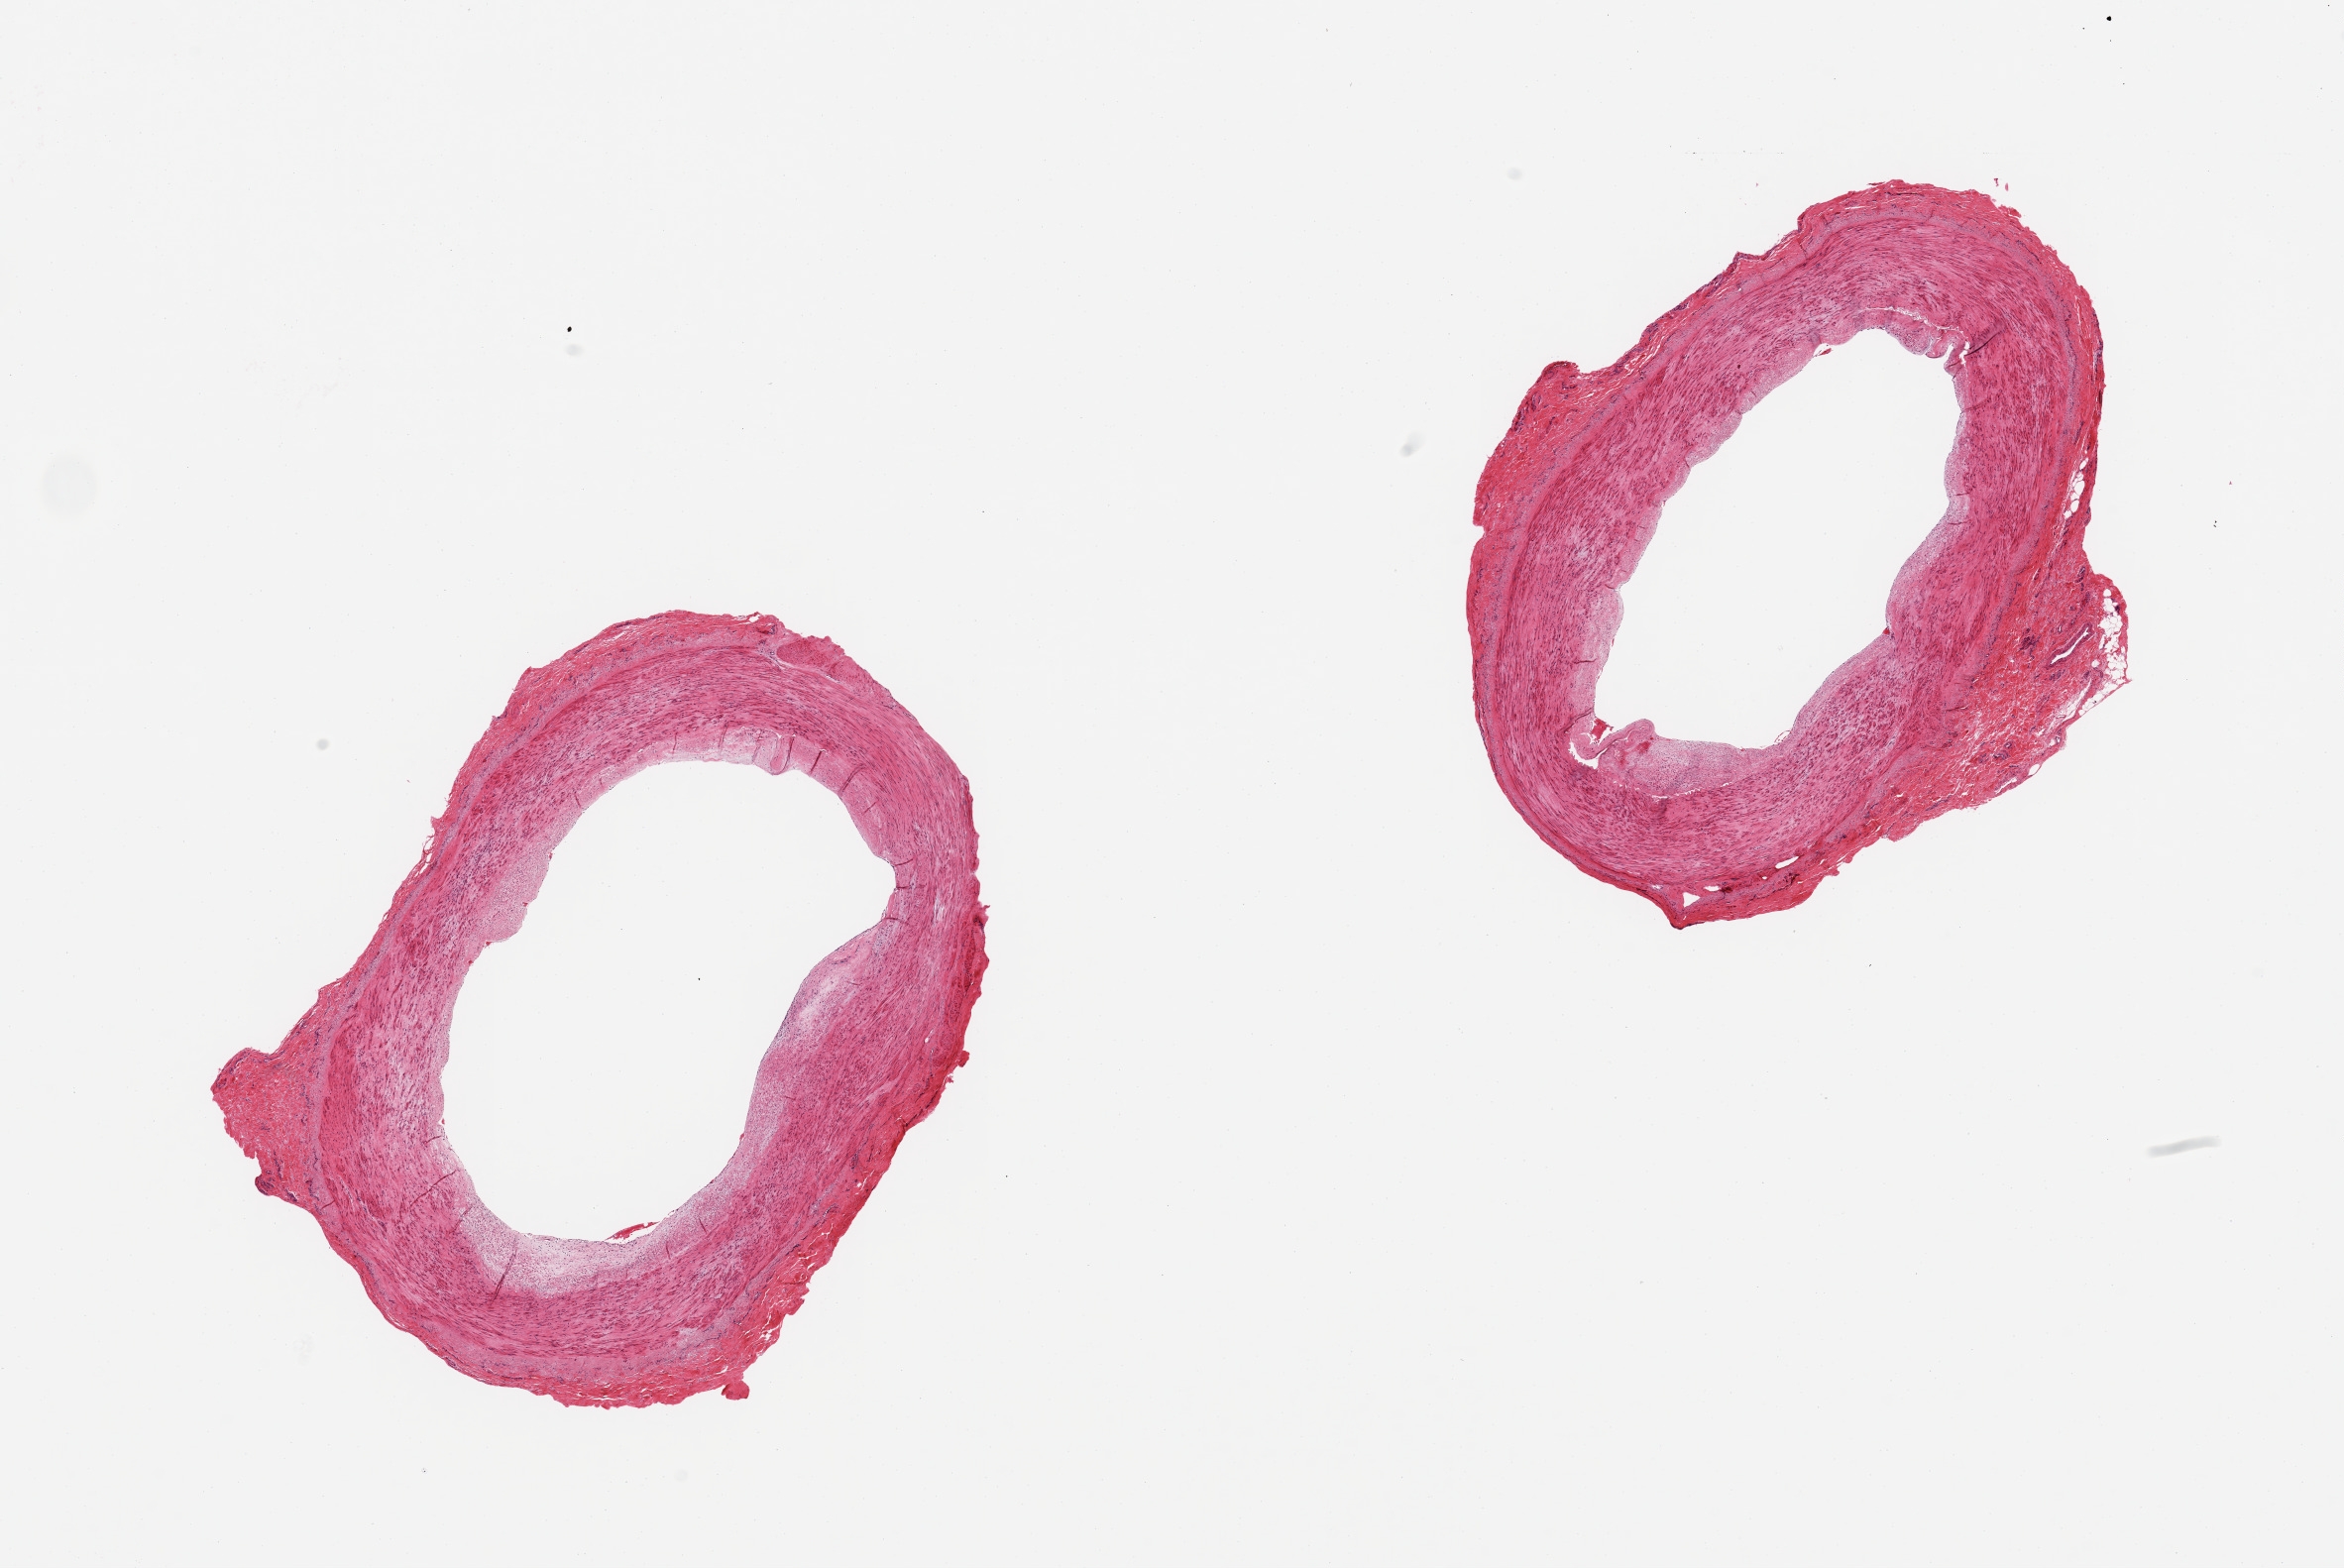
Whole-slide image, haematoxylin and eosin stain, a low-resolution overview of the entire scanned area, about 18.7 x 12.5 mm (acquisition: 20x scan). PAXgene-fixed paraffin-embedded (PFPE) section. Sampled site (target tissue): tibial artery. Tissue donor sample.
Reviewer comment on this tissue sample: 2 pieces, no adherent fat; ~10% occlusive luminal atherosis.